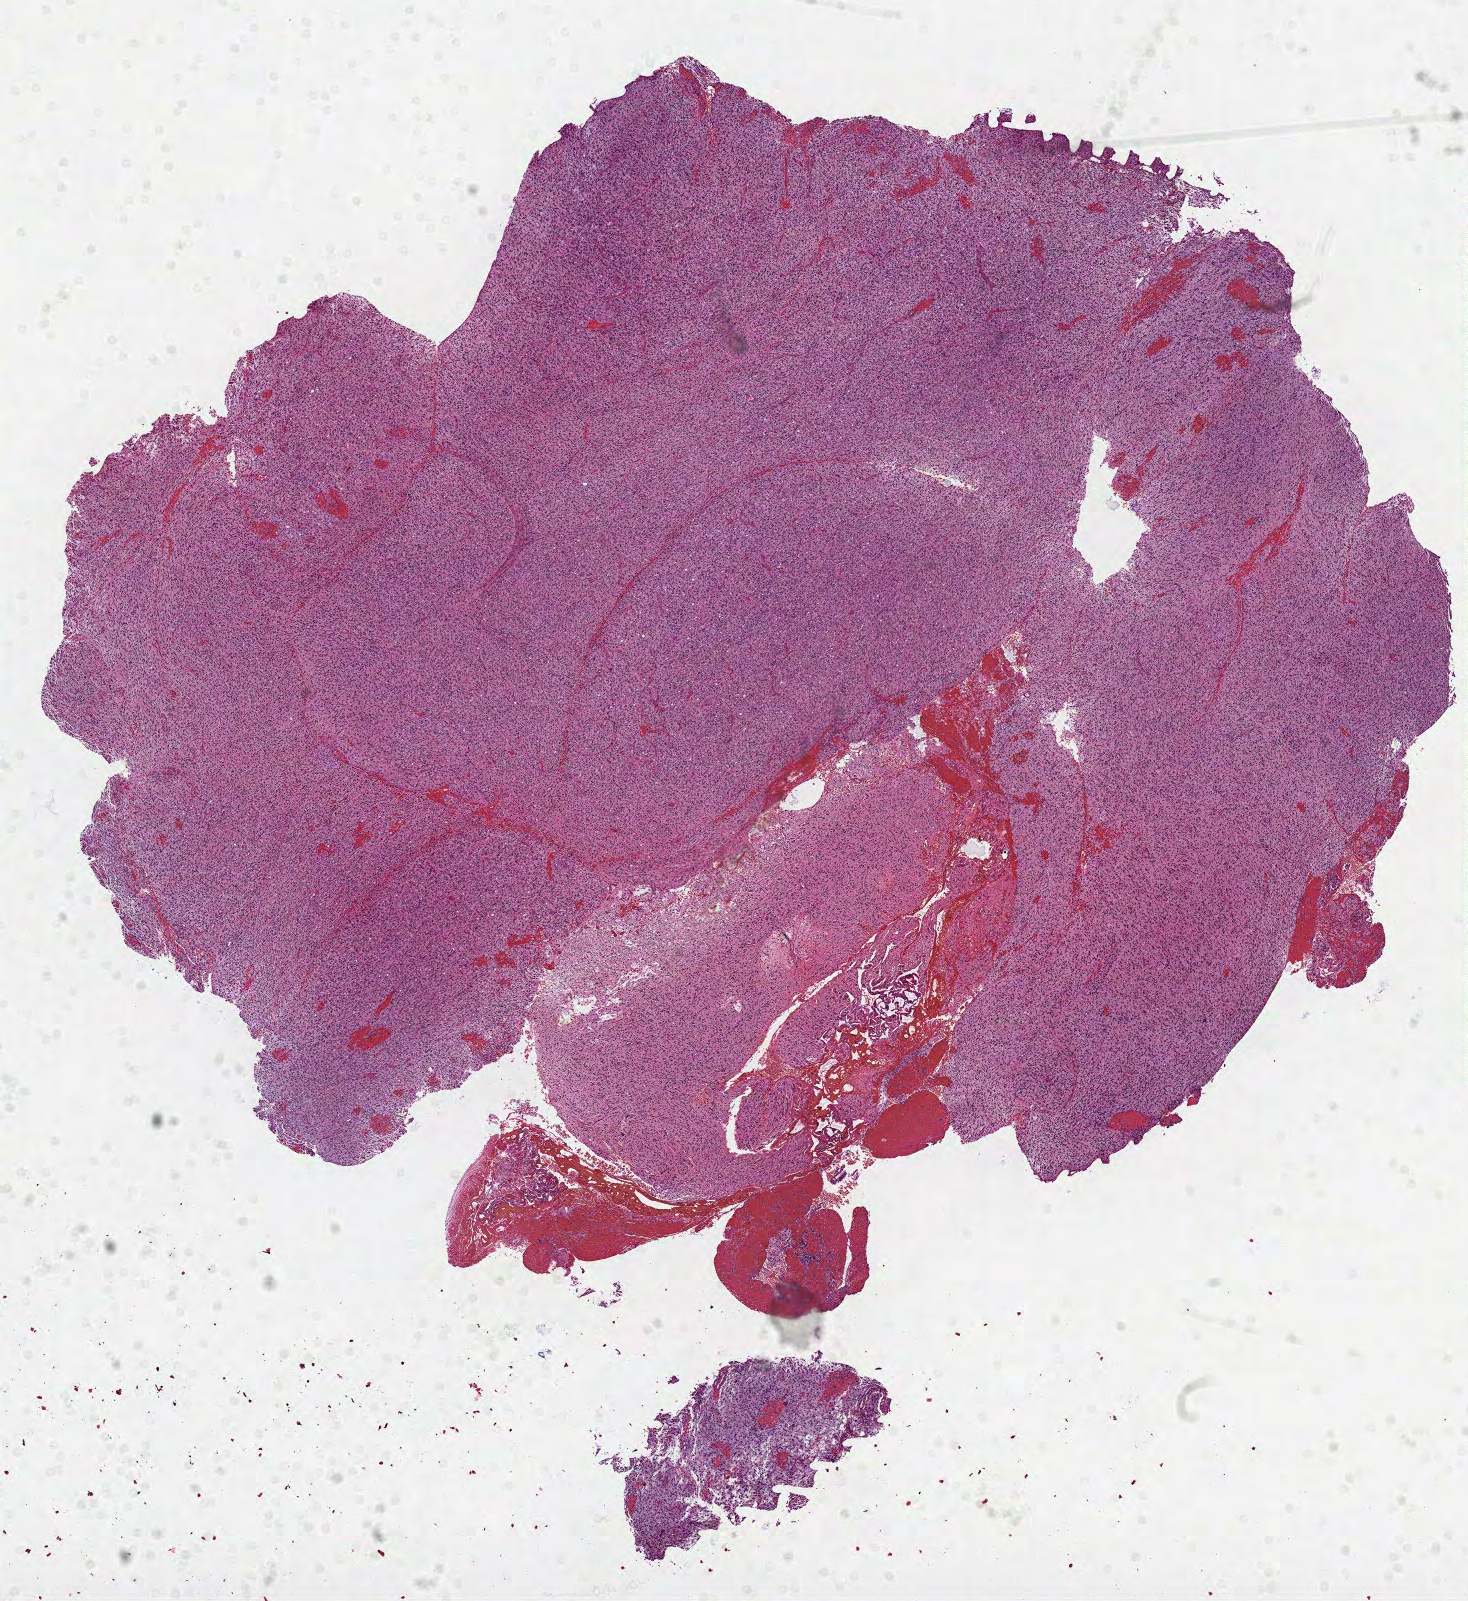
Digitized H&E-stained tissue section (whole slide), a low-resolution overview of the entire scanned area, about 11.8 x 12.9 mm (slide scanned at 40x). Formalin-fixed paraffin-embedded (FFPE) diagnostic section. Brain, primary tumour sample. Male patient; age at initial diagnosis 88 years.
Pathologic diagnosis: Glioblastoma.